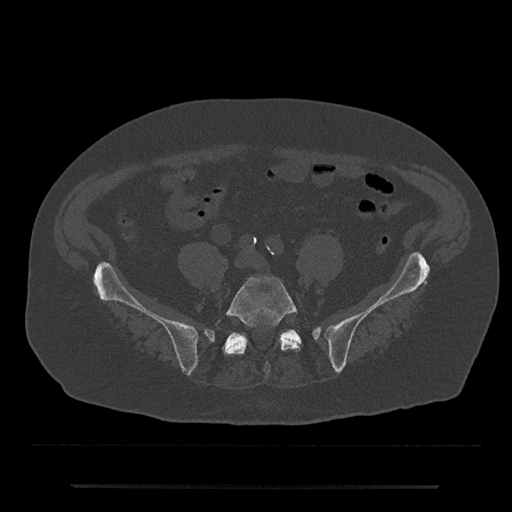
CT including the spine, one axial slice. Slice 275 of 797 in the series (ordered by position). Reconstruction kernel Br40s/3. Bone window (W 1800 / L 400 HU). 0.5 mm slice thickness. 512 × 512 image matrix, field of view 434 × 434 mm. Male patient, age 80 years. From the clinical record (not read from this slice): primary cancer: prostate; vertebrae with lytic lesions (as recorded): L1, T11.
Structures marked on this image (semi-automatic segmentation, software-assisted and operator-edited):
- L5 vertebra: box from (x=223, y=276) to (x=300, y=373) px